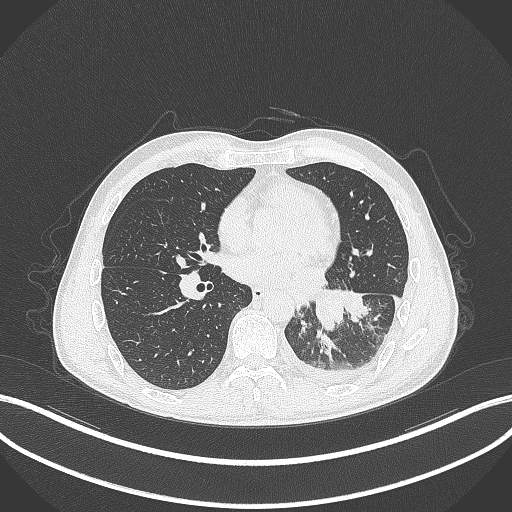
Chest CT, one axial slice; slice 136 of 295 in the series (ordered by position); reconstruction kernel B70f; lung window (W 1500 / L -600 HU); 512 × 512 image matrix. Patient: male, 47 years. From the clinical record (not read from this slice): clinical TNM (as recorded): T3 N1 M1c.
Structures marked on this image (rectangle marked by the reading radiologist):
- lung tumour (recorded histology: small cell carcinoma): bounding box (x1, y1, x2, y2) in pixels: (310, 285, 344, 334)